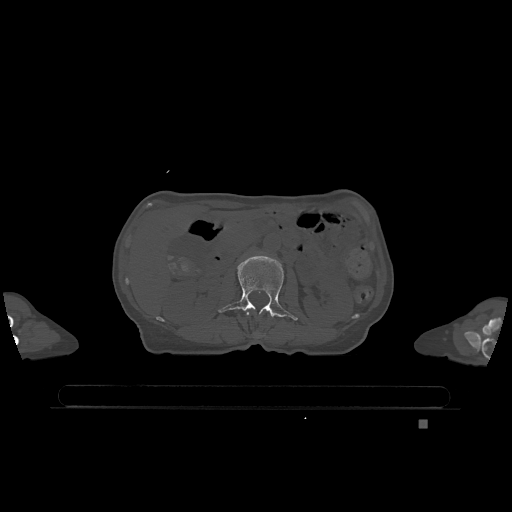
CT including the spine, one axial slice; slice 420 of 1317 in the series (ordered by position); bone window (W 1800 / L 400 HU); 0.5 mm slice thickness; 512 × 512 image matrix. Female patient, age 74 years. Case-level facts recorded for this patient, not image findings: primary cancer: lung.
Structures marked on this image (semi-automatically segmented with operator editing):
- L1 vertebra: bounding box [x1, y1, x2, y2] px = [246, 312, 249, 316]
- L2 vertebra: [218, 256, 298, 321]